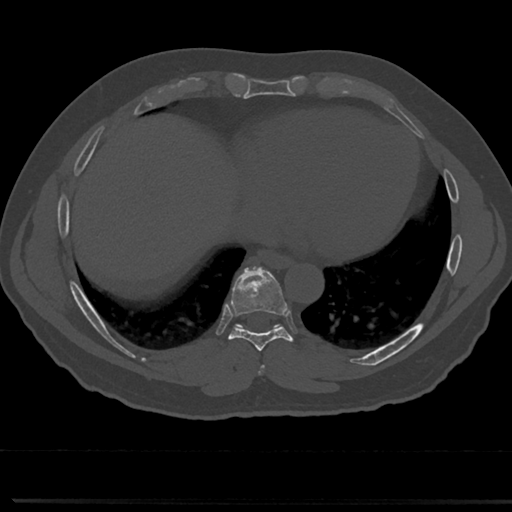
CT including the spine, one axial slice; slice 346 of 817 in the series (ordered by position); reconstruction kernel Br40s/3; bone window (W 1800 / L 400 HU); 512 × 512 image matrix, field of view 355 × 355 mm. Male patient, age 61 years. From the clinical record (not read from this slice): primary cancer: prostate.
Annotated regions visible in this slice (semi-automatic segmentation, software-assisted and operator-edited):
- T7 vertebra: box from (x=255, y=341) to (x=269, y=376) px
- T8 vertebra: (x=216, y=271)–(x=304, y=353)